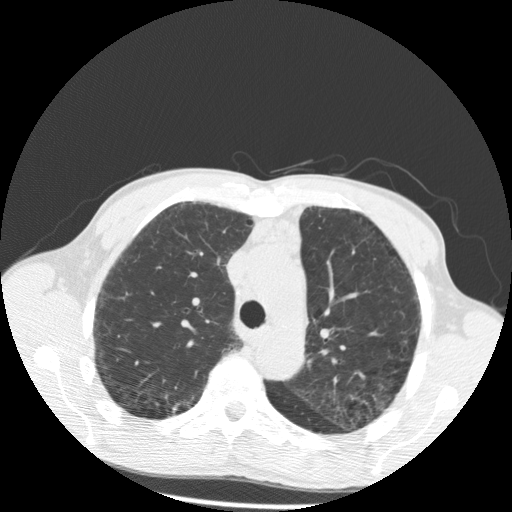
Axial slice from a low-dose chest CT screening exam; baseline screening round; lung window (W 1500 / L -600 HU); 120 kVp; 512 × 512 image matrix. Male, age 60 years at enrolment. Current smoker at enrolment.
Expert reader's lesion annotation, bounding box [x1, y1, x2, y2] px = [159, 397, 189, 426]. Reader record for this screening exam (exam-level; its link to the box is not recorded): non-calcified nodule or mass ≥4 mm, right lower lobe, 6 × 6 mm, spiculated (stellate) margins, soft tissue attenuation. Participant outcome: lung cancer diagnosed 688 days after this screen — squamous cell carcinoma, NOS, right upper lobe, well differentiated (G1), stage IA (AJCC 6th edition), 15 mm at pathology.